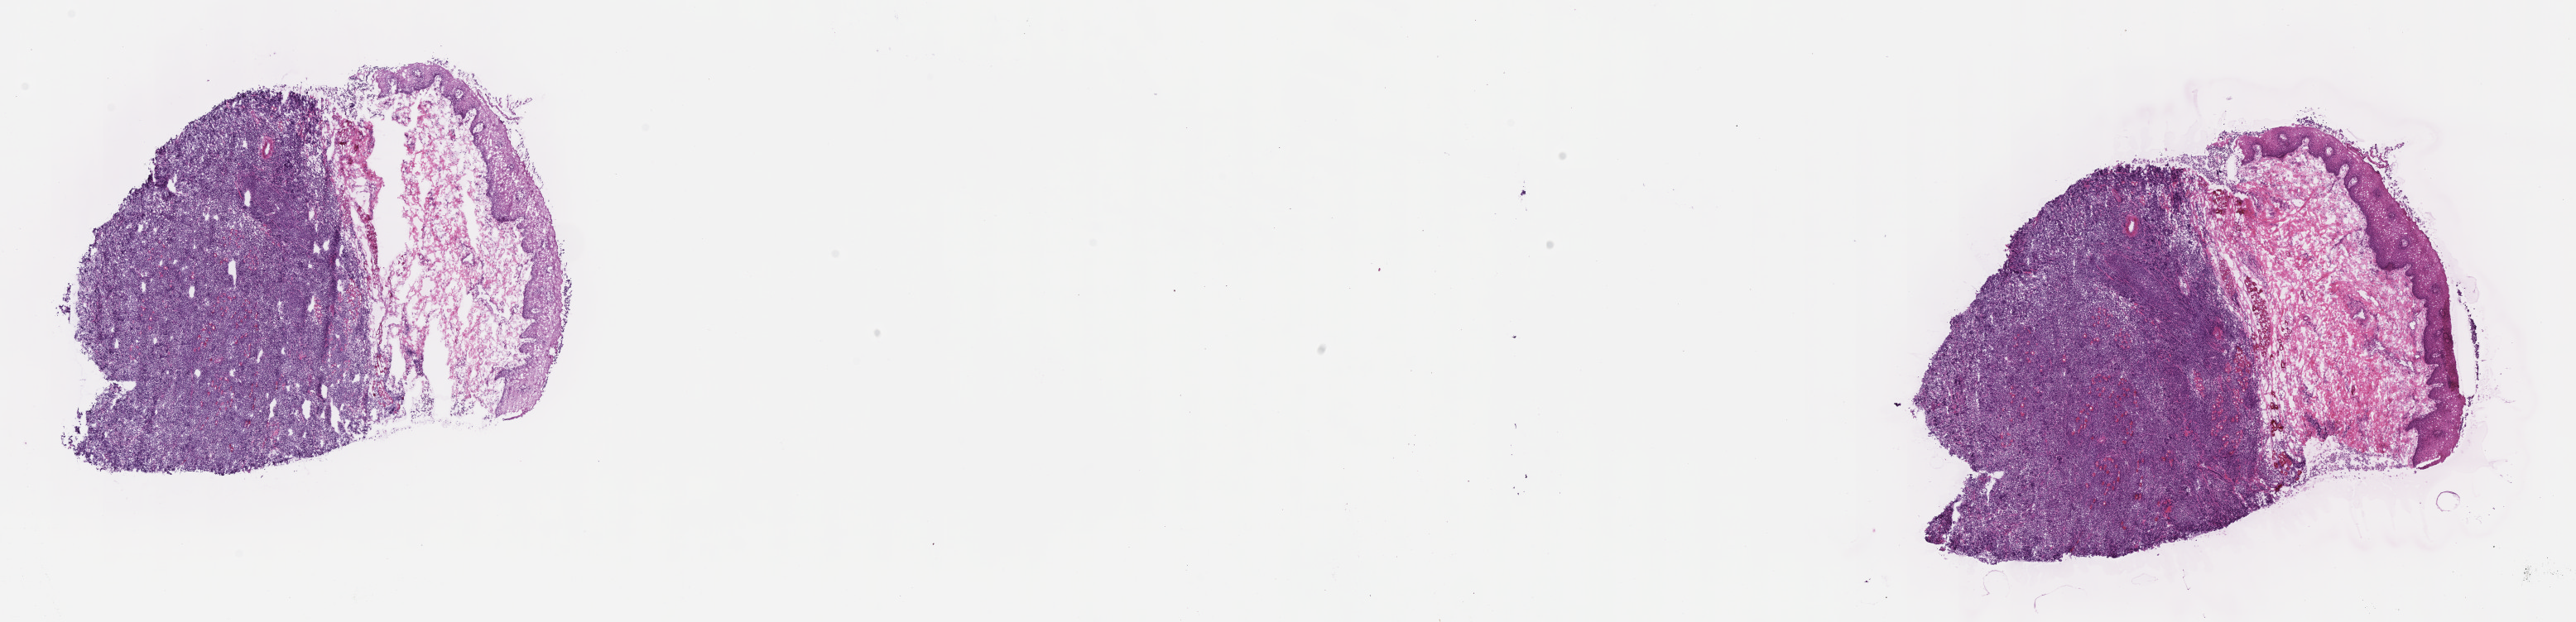
H&E whole-slide image — whole scanned area (about 25.2 x 6.1 mm) shown as a low-resolution overview; frozen section (tissue freezing medium); primary tumor; anatomic site: cranium. Female patient; age at initial diagnosis 6 years. Pathologist review of this section (percent, as recorded): tumor cells 65%, tumor nuclei 80%, stromal cells 35%, necrosis 0%, normal cells 0%. Inflammatory infiltration, as recorded: lymphocyte infiltration 10%, monocyte infiltration 30%, neutrophil infiltration 5%.
Diagnosis: Burkitt lymphoma, NOS. Ann Arbor stage (patient): Stage III. Section: bottom of the tissue portion.